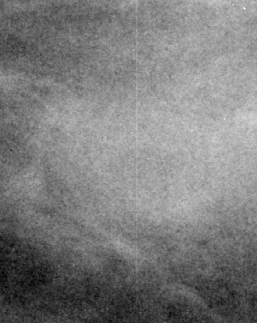
Region of interest cut from a scanned film mammogram (one marked finding); right breast; CC view.
Mass, shape asymmetric breast tissue; BI-RADS assessment category 2; benign; no additional work-up was recommended (benign without callback).